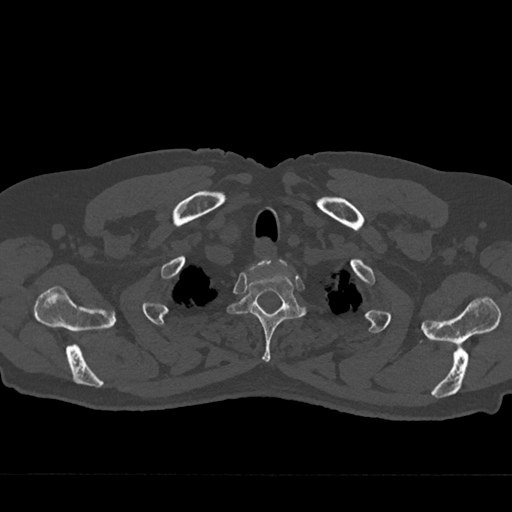
CT including the spine, one axial slice. Position 618 of 797 along the scan axis. Reconstruction kernel Br40s/3. 120 kVp. Bone window (W 1800 / L 400 HU). 0.5 mm slice thickness. 512 × 512 image matrix. Male patient, age 75 years. Case-level facts recorded for this patient, not image findings: primary cancer: renal; vertebrae with lytic lesions (as recorded): T4.
Outlined on this slice (semi-automatic segmentation, software-assisted and operator-edited):
- T1 vertebra: bounding box <249,259,287,272> (left, top, right, bottom; pixels)
- T2 vertebra: <227,262,306,362>